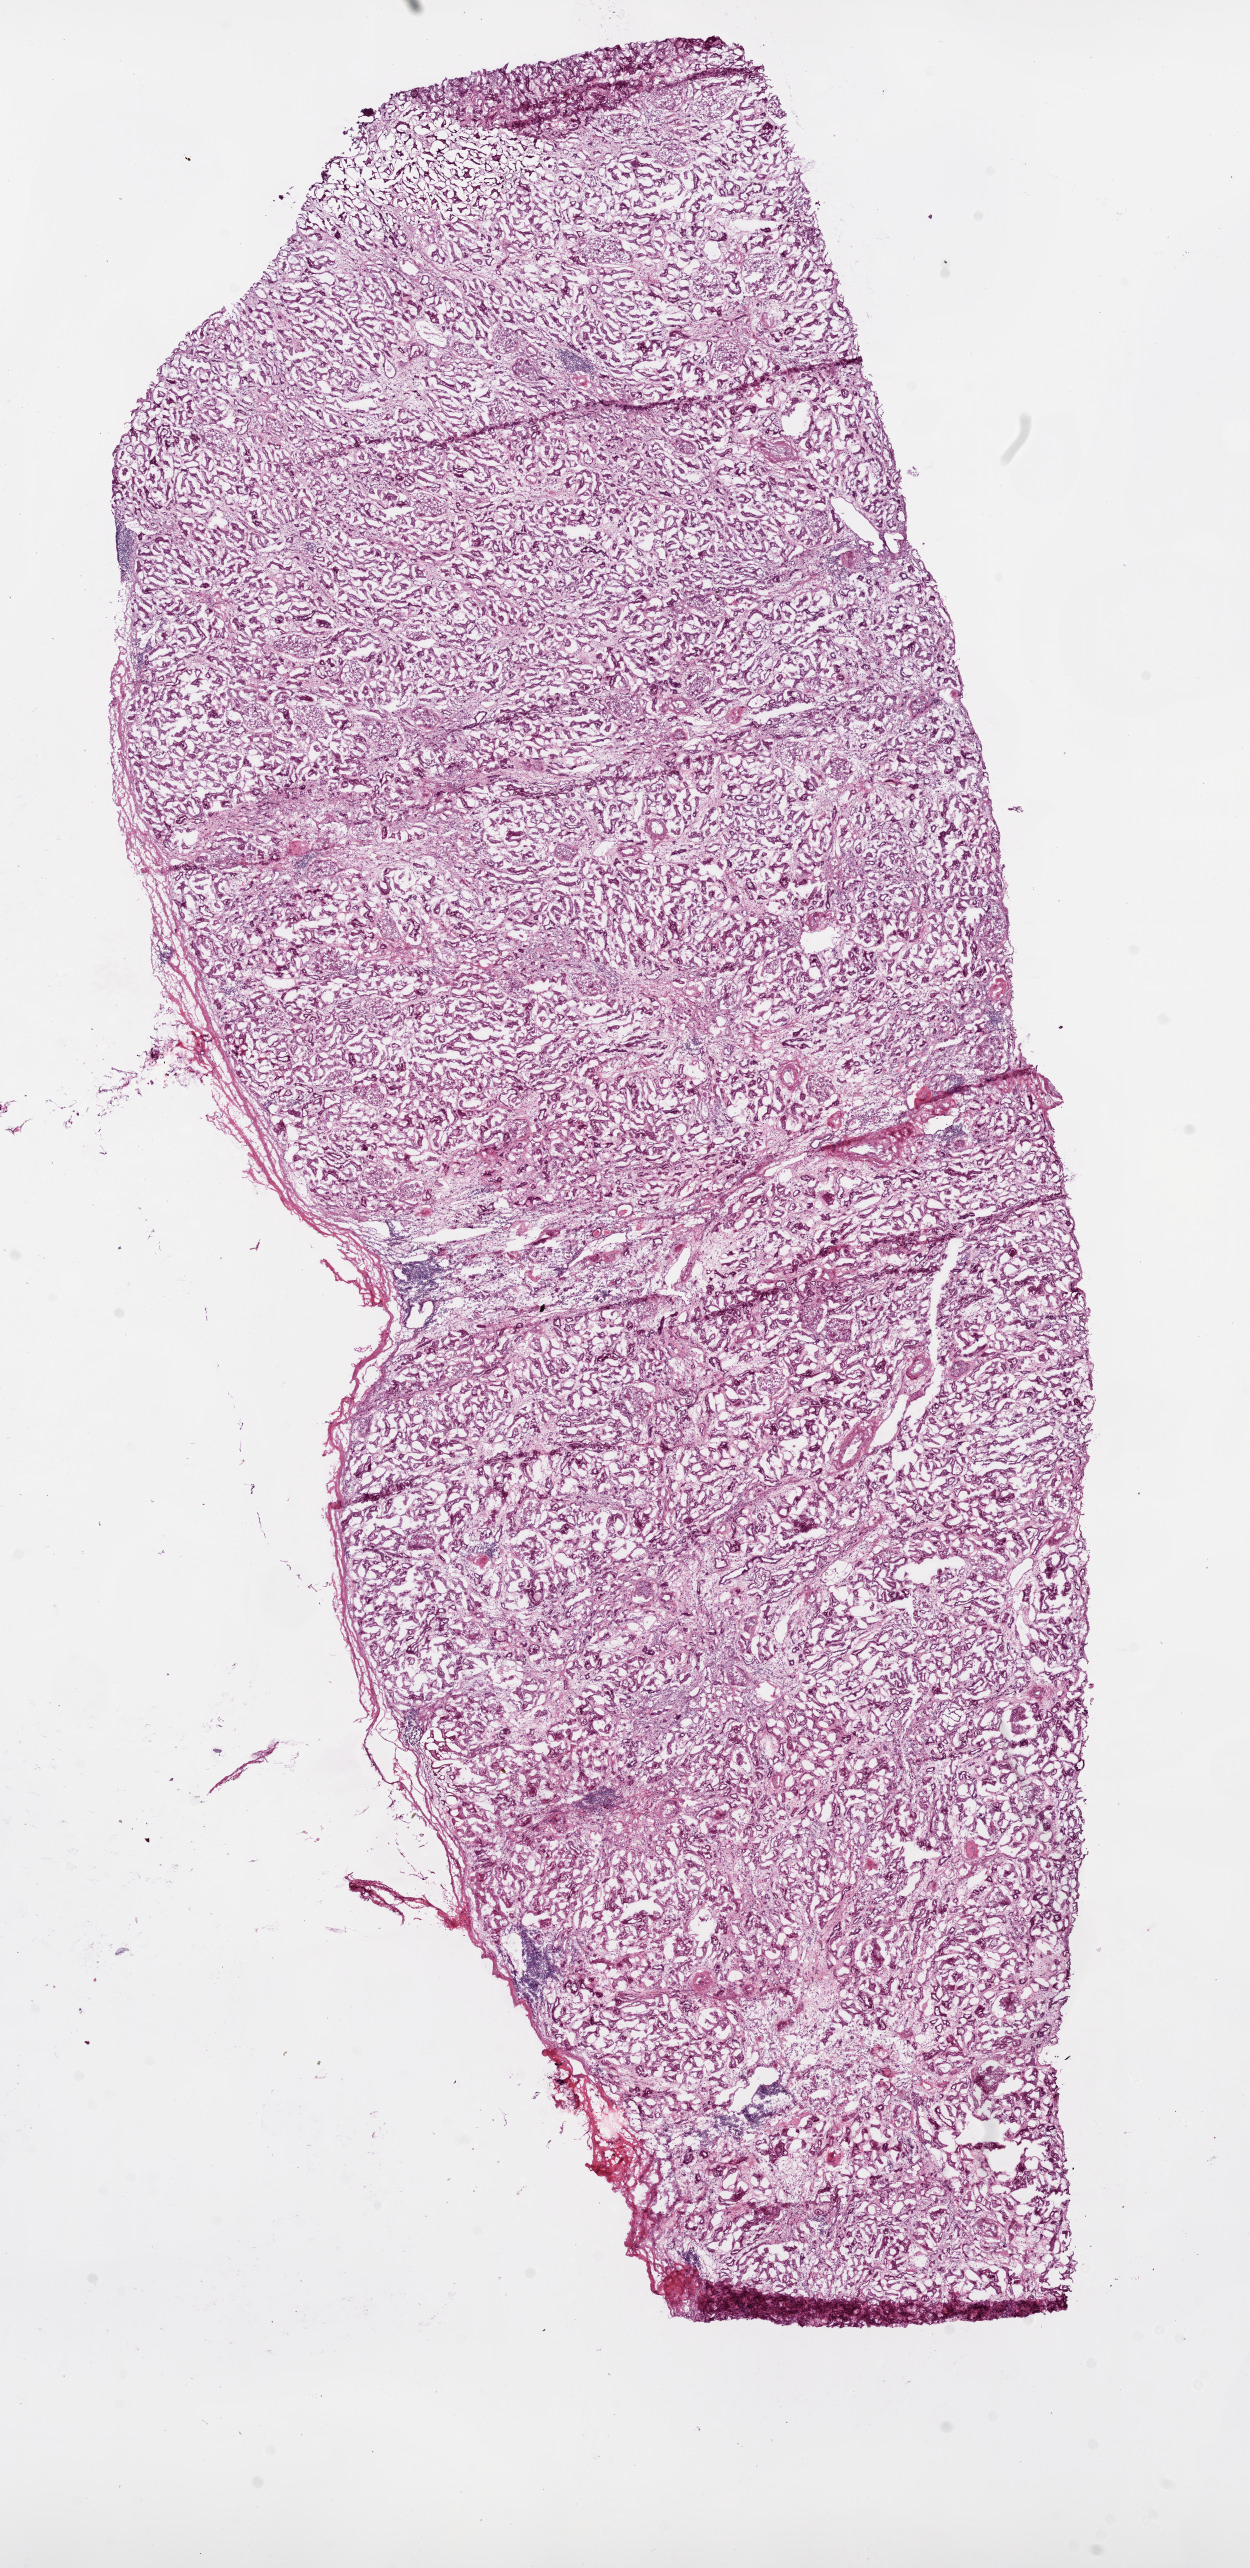
H&E whole-slide image — shown as a low-resolution overview of the whole scanned area (about 10.0 x 20.6 mm); frozen section from the bottom of the tissue portion; sample: solid tissue normal (non-tumour tissue), kidney. Male, age 68 years at initial diagnosis.
This section: solid tissue normal sample (biorepository sample class). Patient diagnosis: Clear cell adenocarcinoma, NOS.